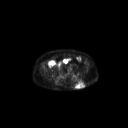
FDG PET of an extremity soft-tissue mass (from a PET/CT study), one axial slice. Slice 78 of 267 in the series (ordered by position). 3.27 mm slice thickness. 128 × 128 image matrix, field of view 700 × 700 mm. Male patient, age 69 years. From the clinical record (not read from this slice): histological type: leiomyosarcoma; grade: intermediate; site of the primary tumour: left pelvis.
Structures marked on this image (expert contour drawn on MRI and transferred to this co-registered scan by the dataset authors):
- gross tumour volume (mass): bounding box <74,79,84,89> (left, top, right, bottom; pixels)